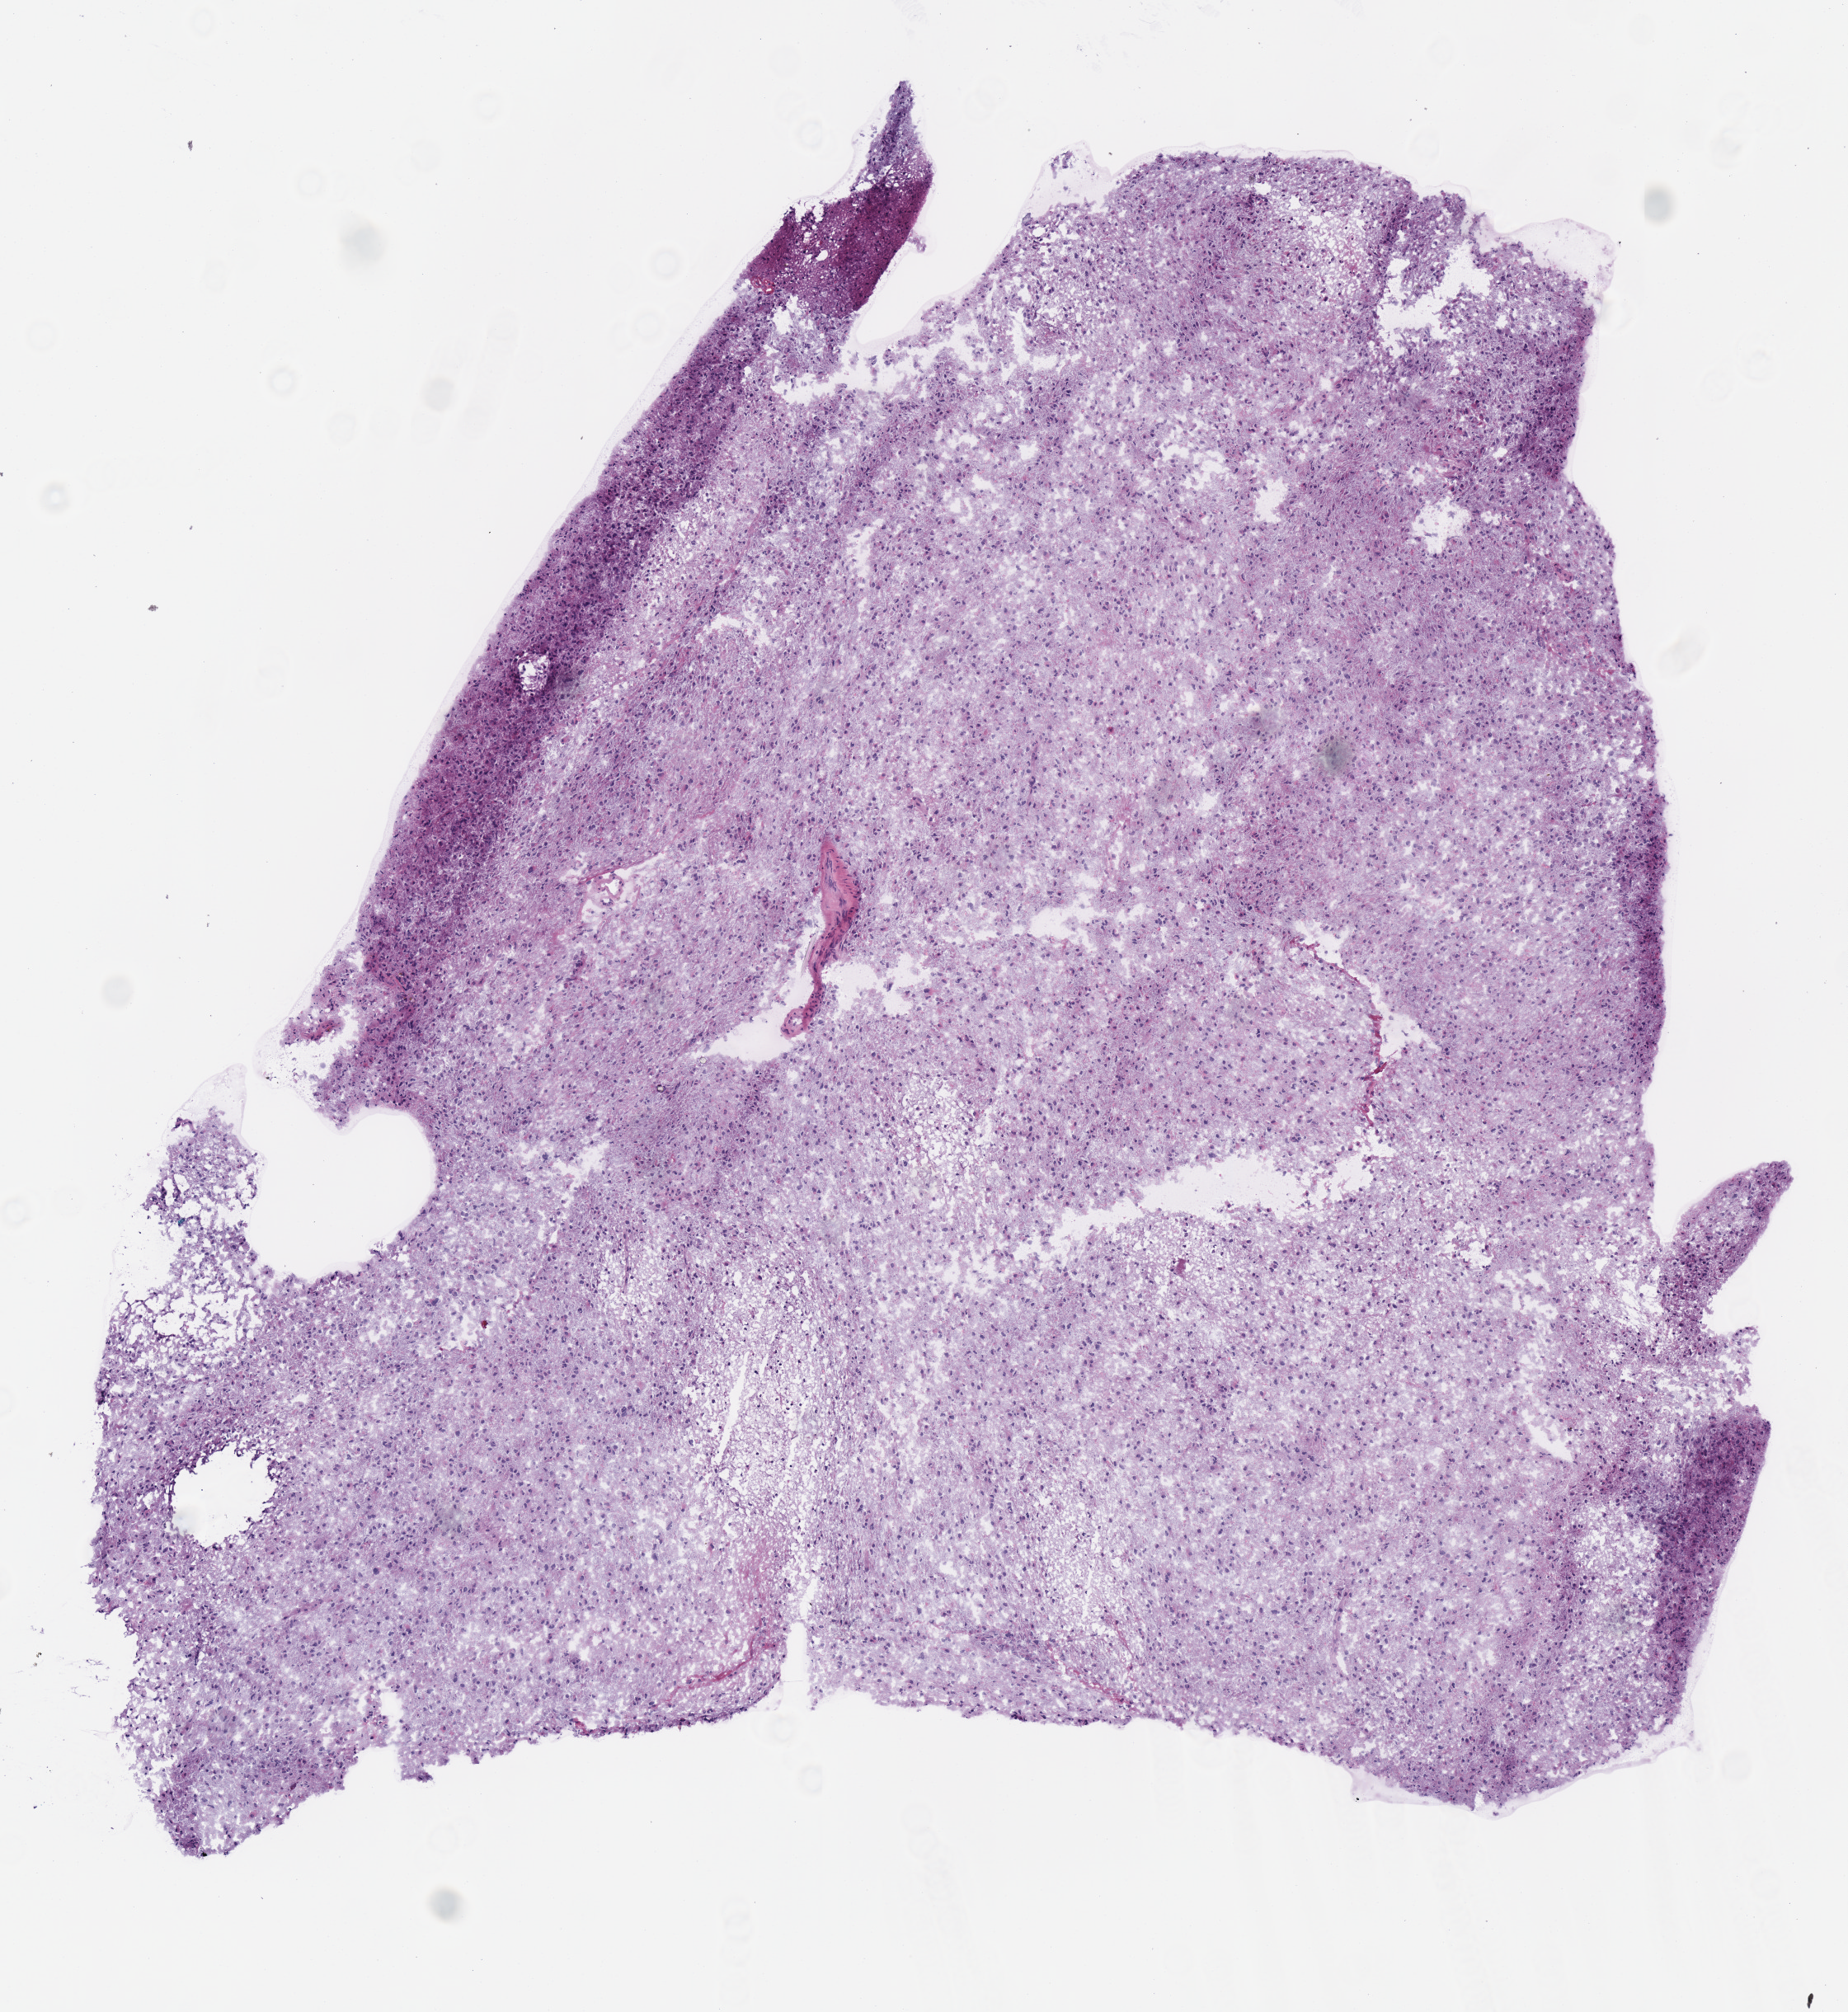
Digitized H&E tissue section (whole slide), shown as a low-resolution overview of the whole scanned area (about 4.4 x 4.8 mm); frozen section from the bottom of the tissue portion; primary tumour sample from the brain. Male, age 26 years at initial diagnosis. Histologic grade: G2 (moderately differentiated). Composition of this section per pathologist review: tumour cells 100%, tumour nuclei 70%, normal cells 0%, stromal cells 0%, necrosis 0%.
Laterality: left. Histologic diagnosis: Oligodendroglioma, NOS (cerebrum).